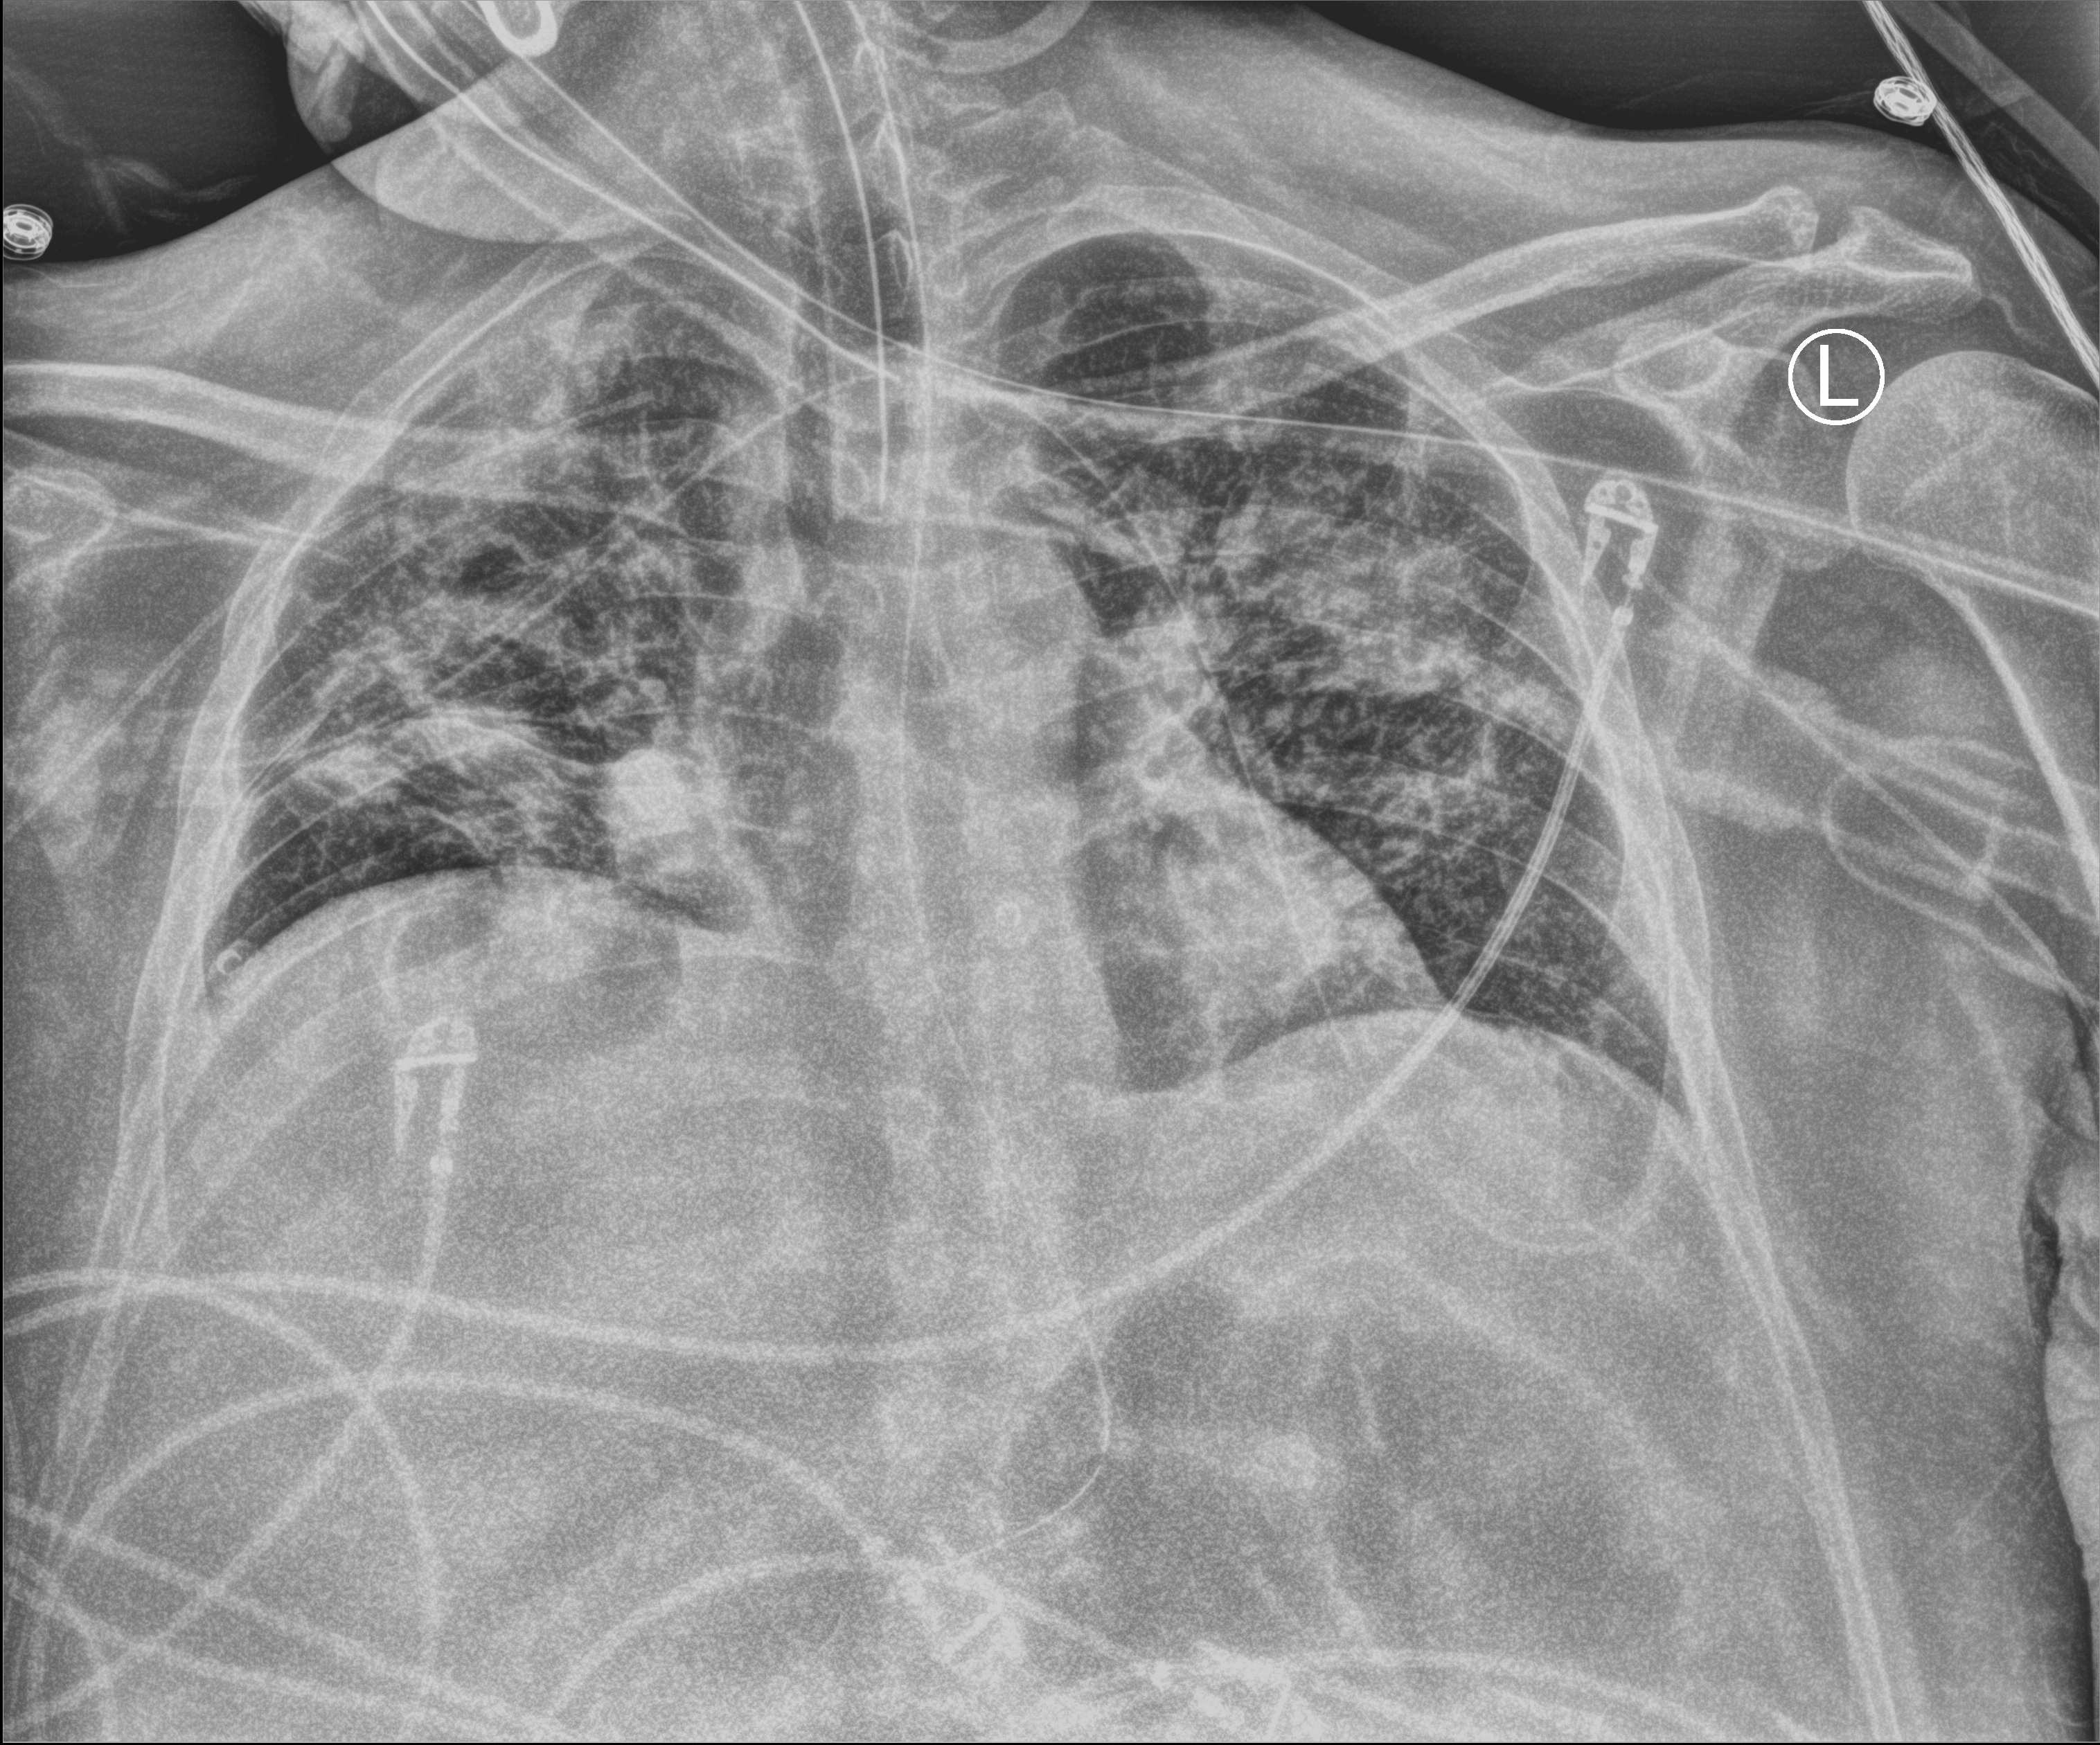
Chest X-ray (portable); anteroposterior (AP) projection. Adult patient hospitalised with COVID-19, age 18–59 years.
From the hospital-stay record, not from the radiograph (when in the stay this image was taken is not recorded): mechanically ventilated during this hospital stay: yes.